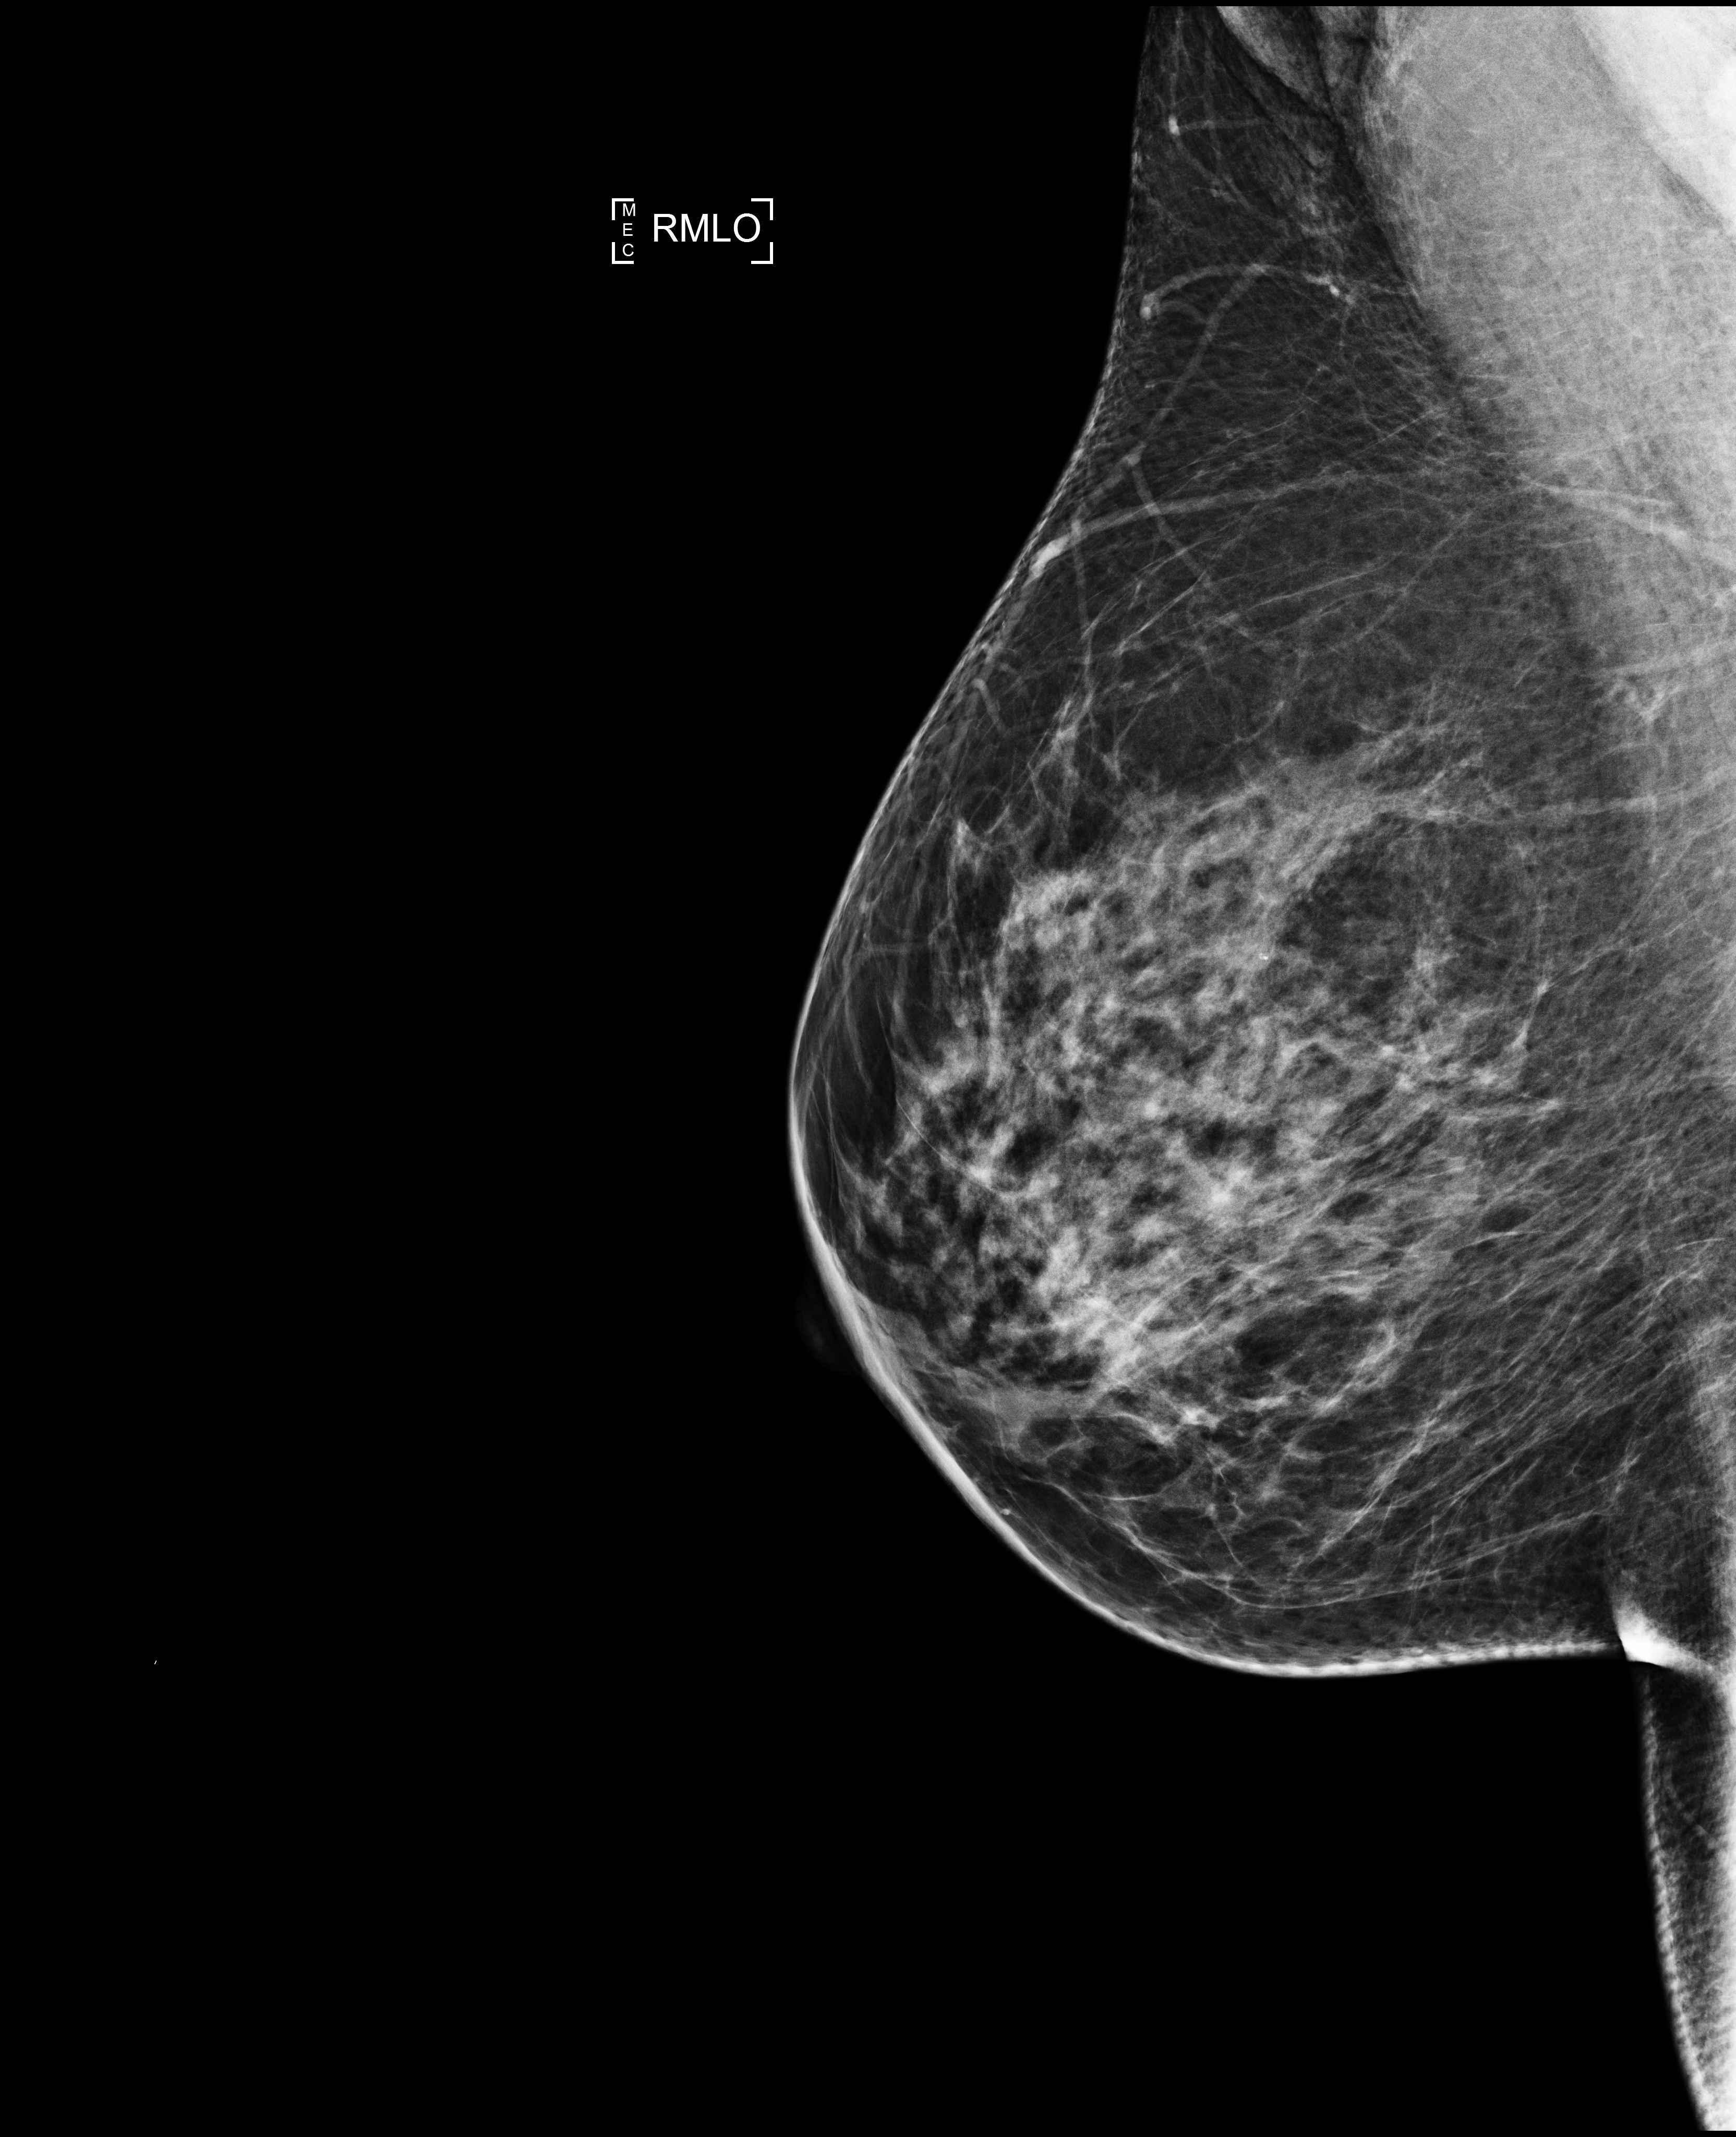
Full-field digital mammogram (FFDM), right breast, medio-lateral oblique projection, annual screening mammography examination, compressed breast thickness 61 mm, system: Selenia Dimensions. Patient aged 46 years (female).
Breast density at the screening exam (both breasts): heterogeneously dense (BI-RADS density category c).